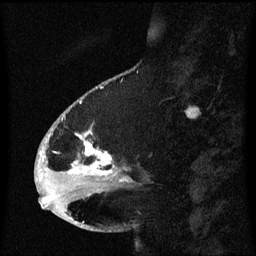
Breast MRI (dynamic contrast-enhanced), one sagittal slice. Slice 23 of 60 in the series (ordered by position). Dynamic contrast-enhanced series, image 2 of 3 at this slice position (ordered by acquisition). 1.5 T. TE 4.2 ms, TR 8.4 ms. 256 × 256 image matrix. Female patient, age 53 years. Case-level facts recorded for this patient, not image findings: setting: breast cancer imaged before/during neoadjuvant chemotherapy; receptor status: HR-positive, HER2-negative.
Structures marked on this image (semi-automatically segmented with operator editing):
- analysis volume of interest (the breast-tissue region the enhancement analysis was run in; not a lesion): bounding box [x1, y1, x2, y2] px = [49, 108, 133, 201]
- tumour enhancement mask (voxels above the 70 % enhancement threshold inside the analysis volume of interest): [70, 130, 113, 175]